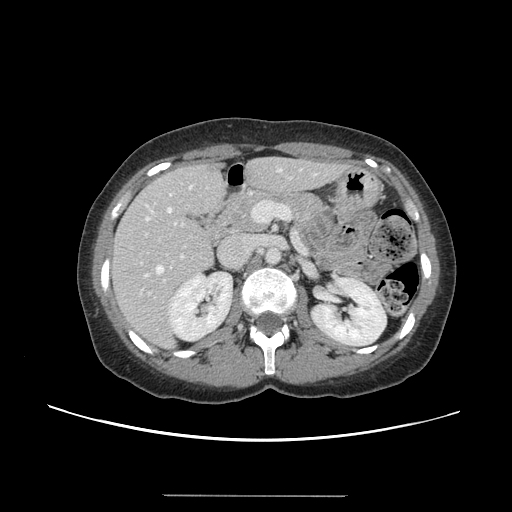
Contrast-enhanced abdominal CT, one axial slice. Slice 72 of 144 in the series (ordered by position). 120 kVp. Soft-tissue window (W 400 / L 40 HU). 2.5 mm slice thickness. 512 × 512 image matrix, field of view 380 × 380 mm. Female patient, age 53 years. From the clinical record (not read from this slice): diagnosis: colorectal cancer liver metastases, imaged before liver resection; multiple liver metastases: yes; largest metastasis: 1.1 cm; chemotherapy before resection: no.
Outlined on this slice (expert manual segmentation):
- hepatic veins: box from (x=145, y=169) to (x=282, y=277) px
- liver: (x=111, y=159)–(x=341, y=346)
- planned liver remnant (the part of the liver to remain after resection): (x=111, y=159)–(x=321, y=301)
- portal vein (with intrahepatic branches): (x=141, y=201)–(x=291, y=295)